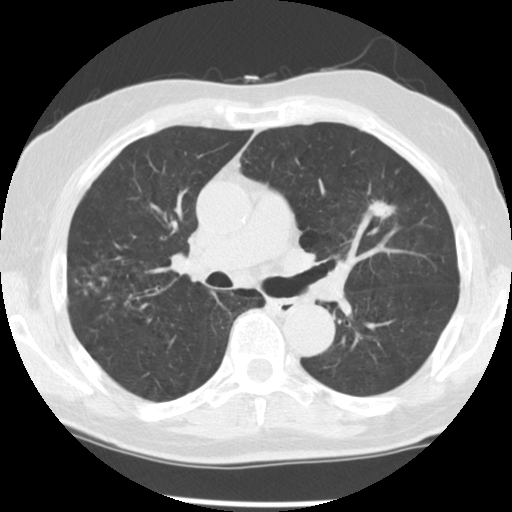
Low-dose screening chest CT, axial slice, third annual screen, lung window (W 1500 / L -600 HU), standard (soft-tissue) reconstruction kernel (STANDARD), 140 kVp, slice 77 of 131 in the series. Male, age 70 years at enrolment. Current smoker at enrolment.
Expert-annotated lung lesion, bounding box (x1, y1, x2, y2) in pixels: (356, 185, 411, 242). The screening reader recorded 3 non-calcified nodules or masses ≥4 mm on this exam (left upper lobe, left upper lobe, right lower lobe); which of them this box marks is not recorded. Official screen result: positive, other.